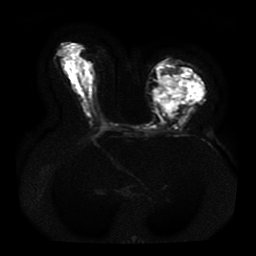
Breast MRI, one axial slice. Position 22 of 41 along the scan axis. Diffusion-weighted series; image 2 of 4 stored at this slice position (different b-values; order by instance number). 1.5 T. 5 mm slice thickness. 256 × 256 image matrix. Female patient.
Annotated regions visible in this slice (outlined manually by an expert reader):
- tumour on diffusion-weighted imaging: bounding box <154,69,203,112> (left, top, right, bottom; pixels)